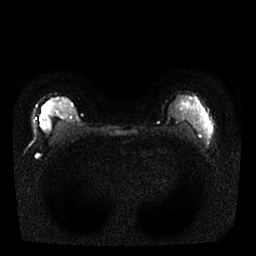
Breast MRI, one axial slice. Slice 14 of 25 in the series (ordered by position). Diffusion-weighted series; image 2 of 4 stored at this slice position (different b-values; order by instance number). 1.5 T. 4 mm slice thickness. 256 × 256 image matrix, field of view 310 × 310 mm. Female patient.
Outlined on this slice (manually delineated by an expert):
- tumour on diffusion-weighted imaging: bounding box <41,122,47,129> (left, top, right, bottom; pixels)